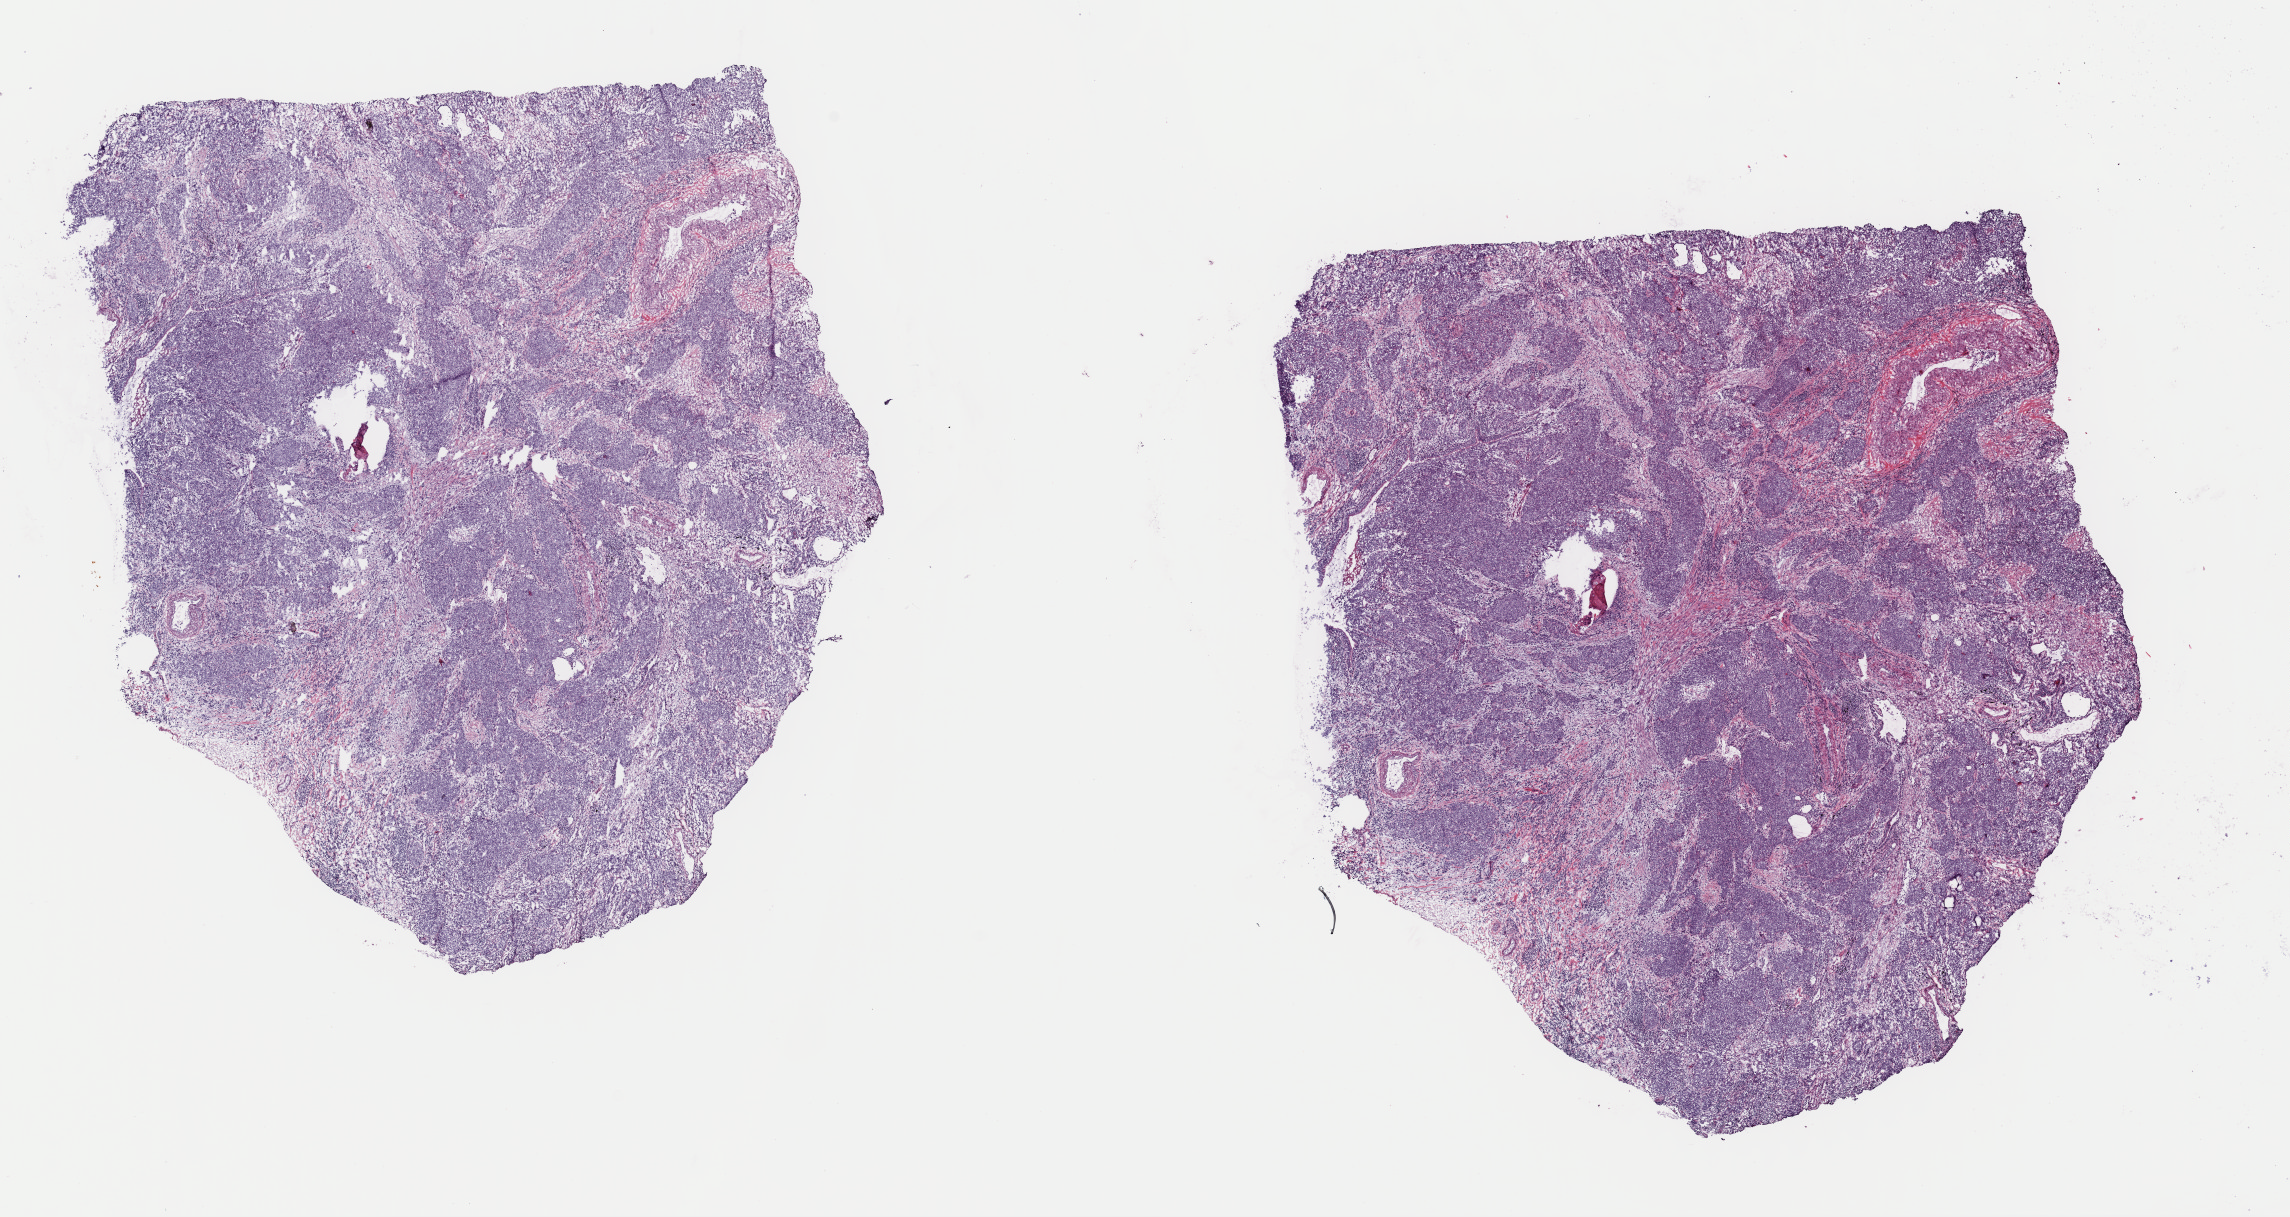
Digitized Hematoxylin and eosin (H&E) stained tissue section (whole slide), low-resolution overview of the scanned area, about 18.1 x 9.6 mm. Frozen section from the top of the tissue portion. Lung, primary tumour sample. Patient: female, age at initial diagnosis 78 years. Pathologist review of this section (percent, as recorded): tumour cells 100%, tumour nuclei 80%, normal cells 0%, stromal cells 0%, necrosis 0%. Infiltration values recorded for this section: lymphocyte infiltration 3%, monocyte infiltration 0%, neutrophil infiltration 0%.
- AJCC pathologic stage: IIA (7th edition)
- TNM: T2a N1 M0
- pathologic diagnosis: Squamous cell carcinoma, NOS (lower lobe, lung)
- laterality: left